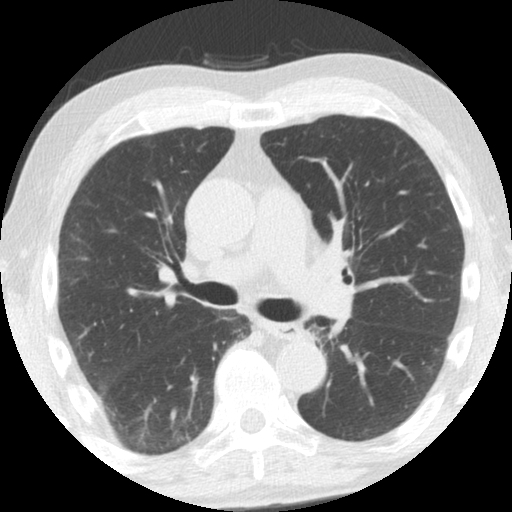
Axial slice from a low-dose chest CT screening exam, third screening round (two years after baseline), lung window (W 1500 / L -600 HU), 2.5 mm slice thickness, 512 × 512 image matrix, field of view 308 × 308 mm. Male participant, aged 61 years at enrolment.
• Expert-annotated lung lesion, bounding box <292,316,344,362> (left, top, right, bottom; pixels).
• No non-calcified nodule or mass ≥4 mm was recorded by the screening reader at this exam.
• Later outcome: lung cancer diagnosed 363 days after this screen — squamous cell carcinoma, NOS, left upper lobe, left lower lobe, well differentiated (G1), stage IIB (AJCC 6th edition), 100 mm at pathology.